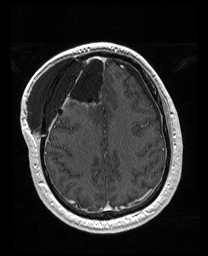
Brain MRI from a brain-tumour surgery series, one axial slice; position 61 of 176 along the scan axis; T1-weighted post-contrast; 1 mm slice thickness; 208 × 256 image matrix, field of view 208 × 256 mm. From the clinical record (not read from this slice): histopathology: Astrocytoma; WHO grade: 4; IDH mutation: yes; tumour location: Right Orbitofrontal Anterior Temporal Insular.
Outlined on this slice (expert manual segmentation):
- previous resection cavity: bounding box <56,53,106,100> (left, top, right, bottom; pixels)